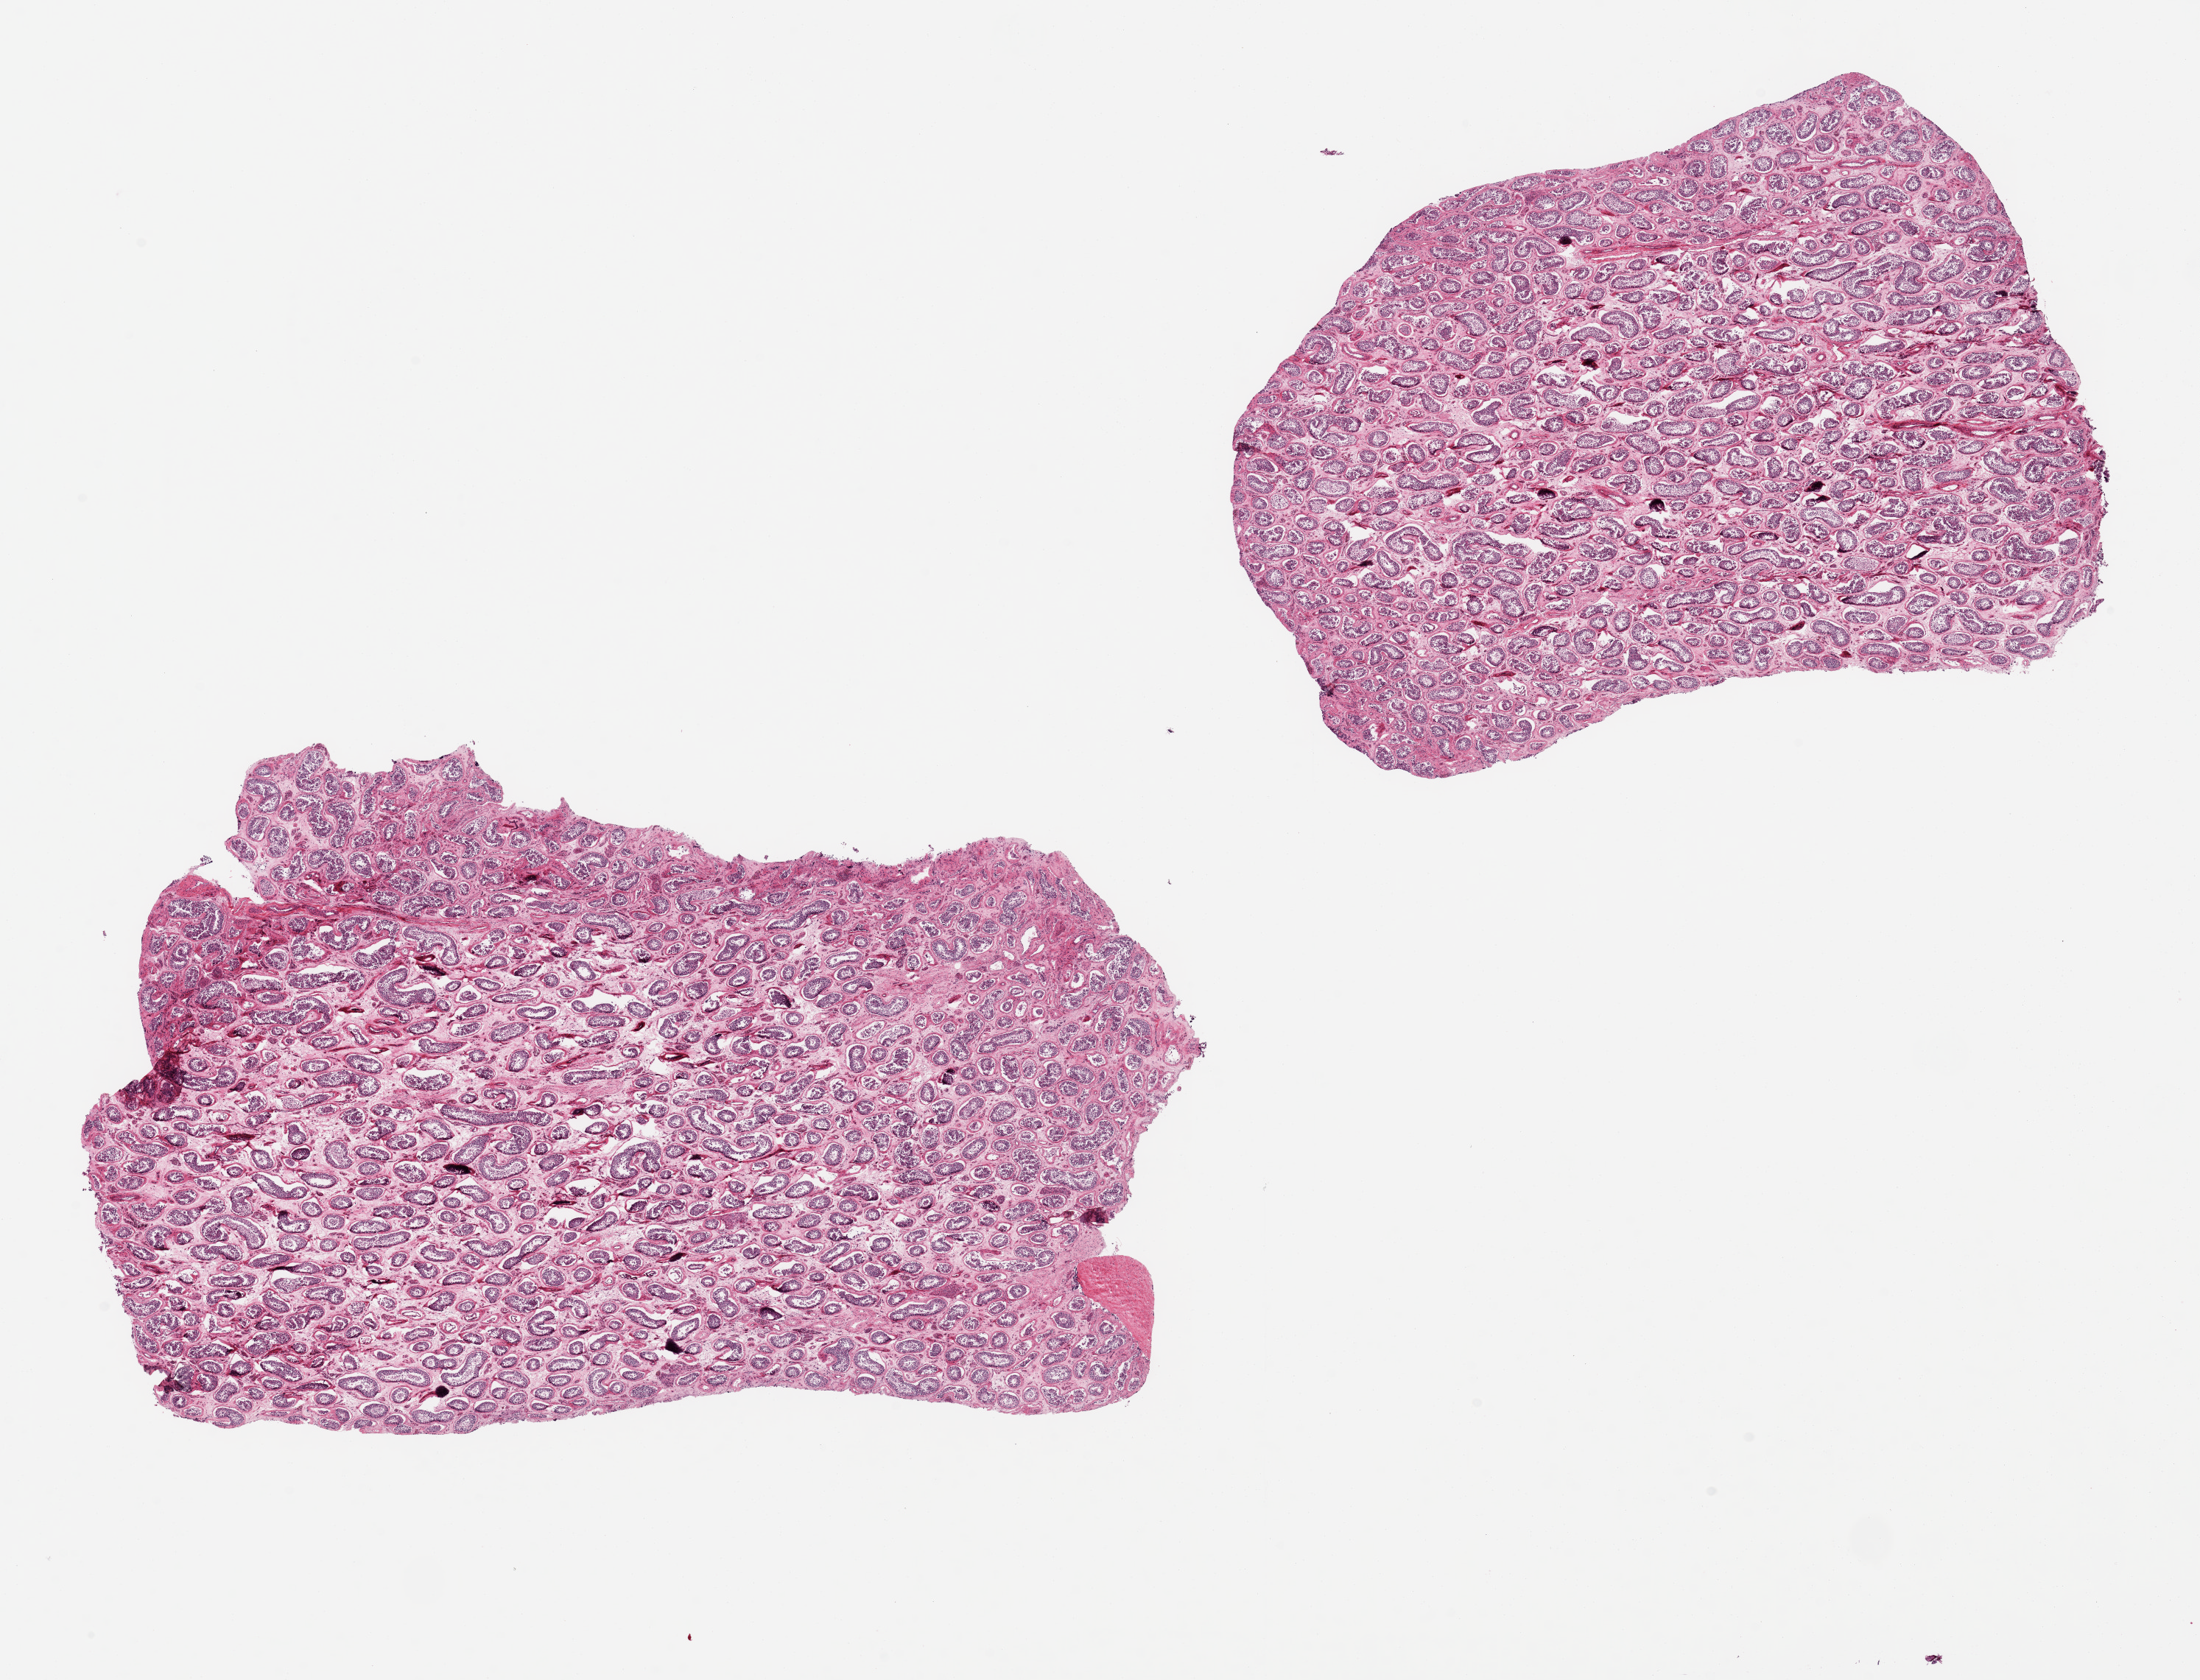
Digitized H&E-stained section, brightfield — a low-resolution overview of the entire scanned area, about 23.6 x 18.0 mm, PAXgene-fixed paraffin-embedded (PFPE) section, target tissue: testis, tissue donor sample. Male donor.
* review note (as recorded): 2 aliquots, ~10x7mm. Reduced spermatogeneisis